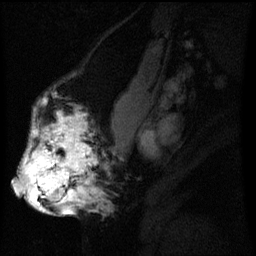
Breast MRI (dynamic contrast-enhanced), one sagittal slice; position 28 of 60 along the scan axis; dynamic contrast-enhanced series, image 2 of 3 at this slice position (ordered by acquisition); 1.5 T; TE 4.2 ms, TR 8 ms; 2.2 mm slice thickness; 256 × 256 image matrix, field of view 200 × 200 mm. Patient: female, 50 years.
Structures marked on this image (semi-automatically segmented with operator editing):
- analysis volume of interest (the breast-tissue region the enhancement analysis was run in; not a lesion): bounding box [x1, y1, x2, y2] px = [20, 112, 97, 211]
- tumour enhancement mask (voxels above the 70 % enhancement threshold inside the analysis volume of interest): [22, 116, 90, 211]